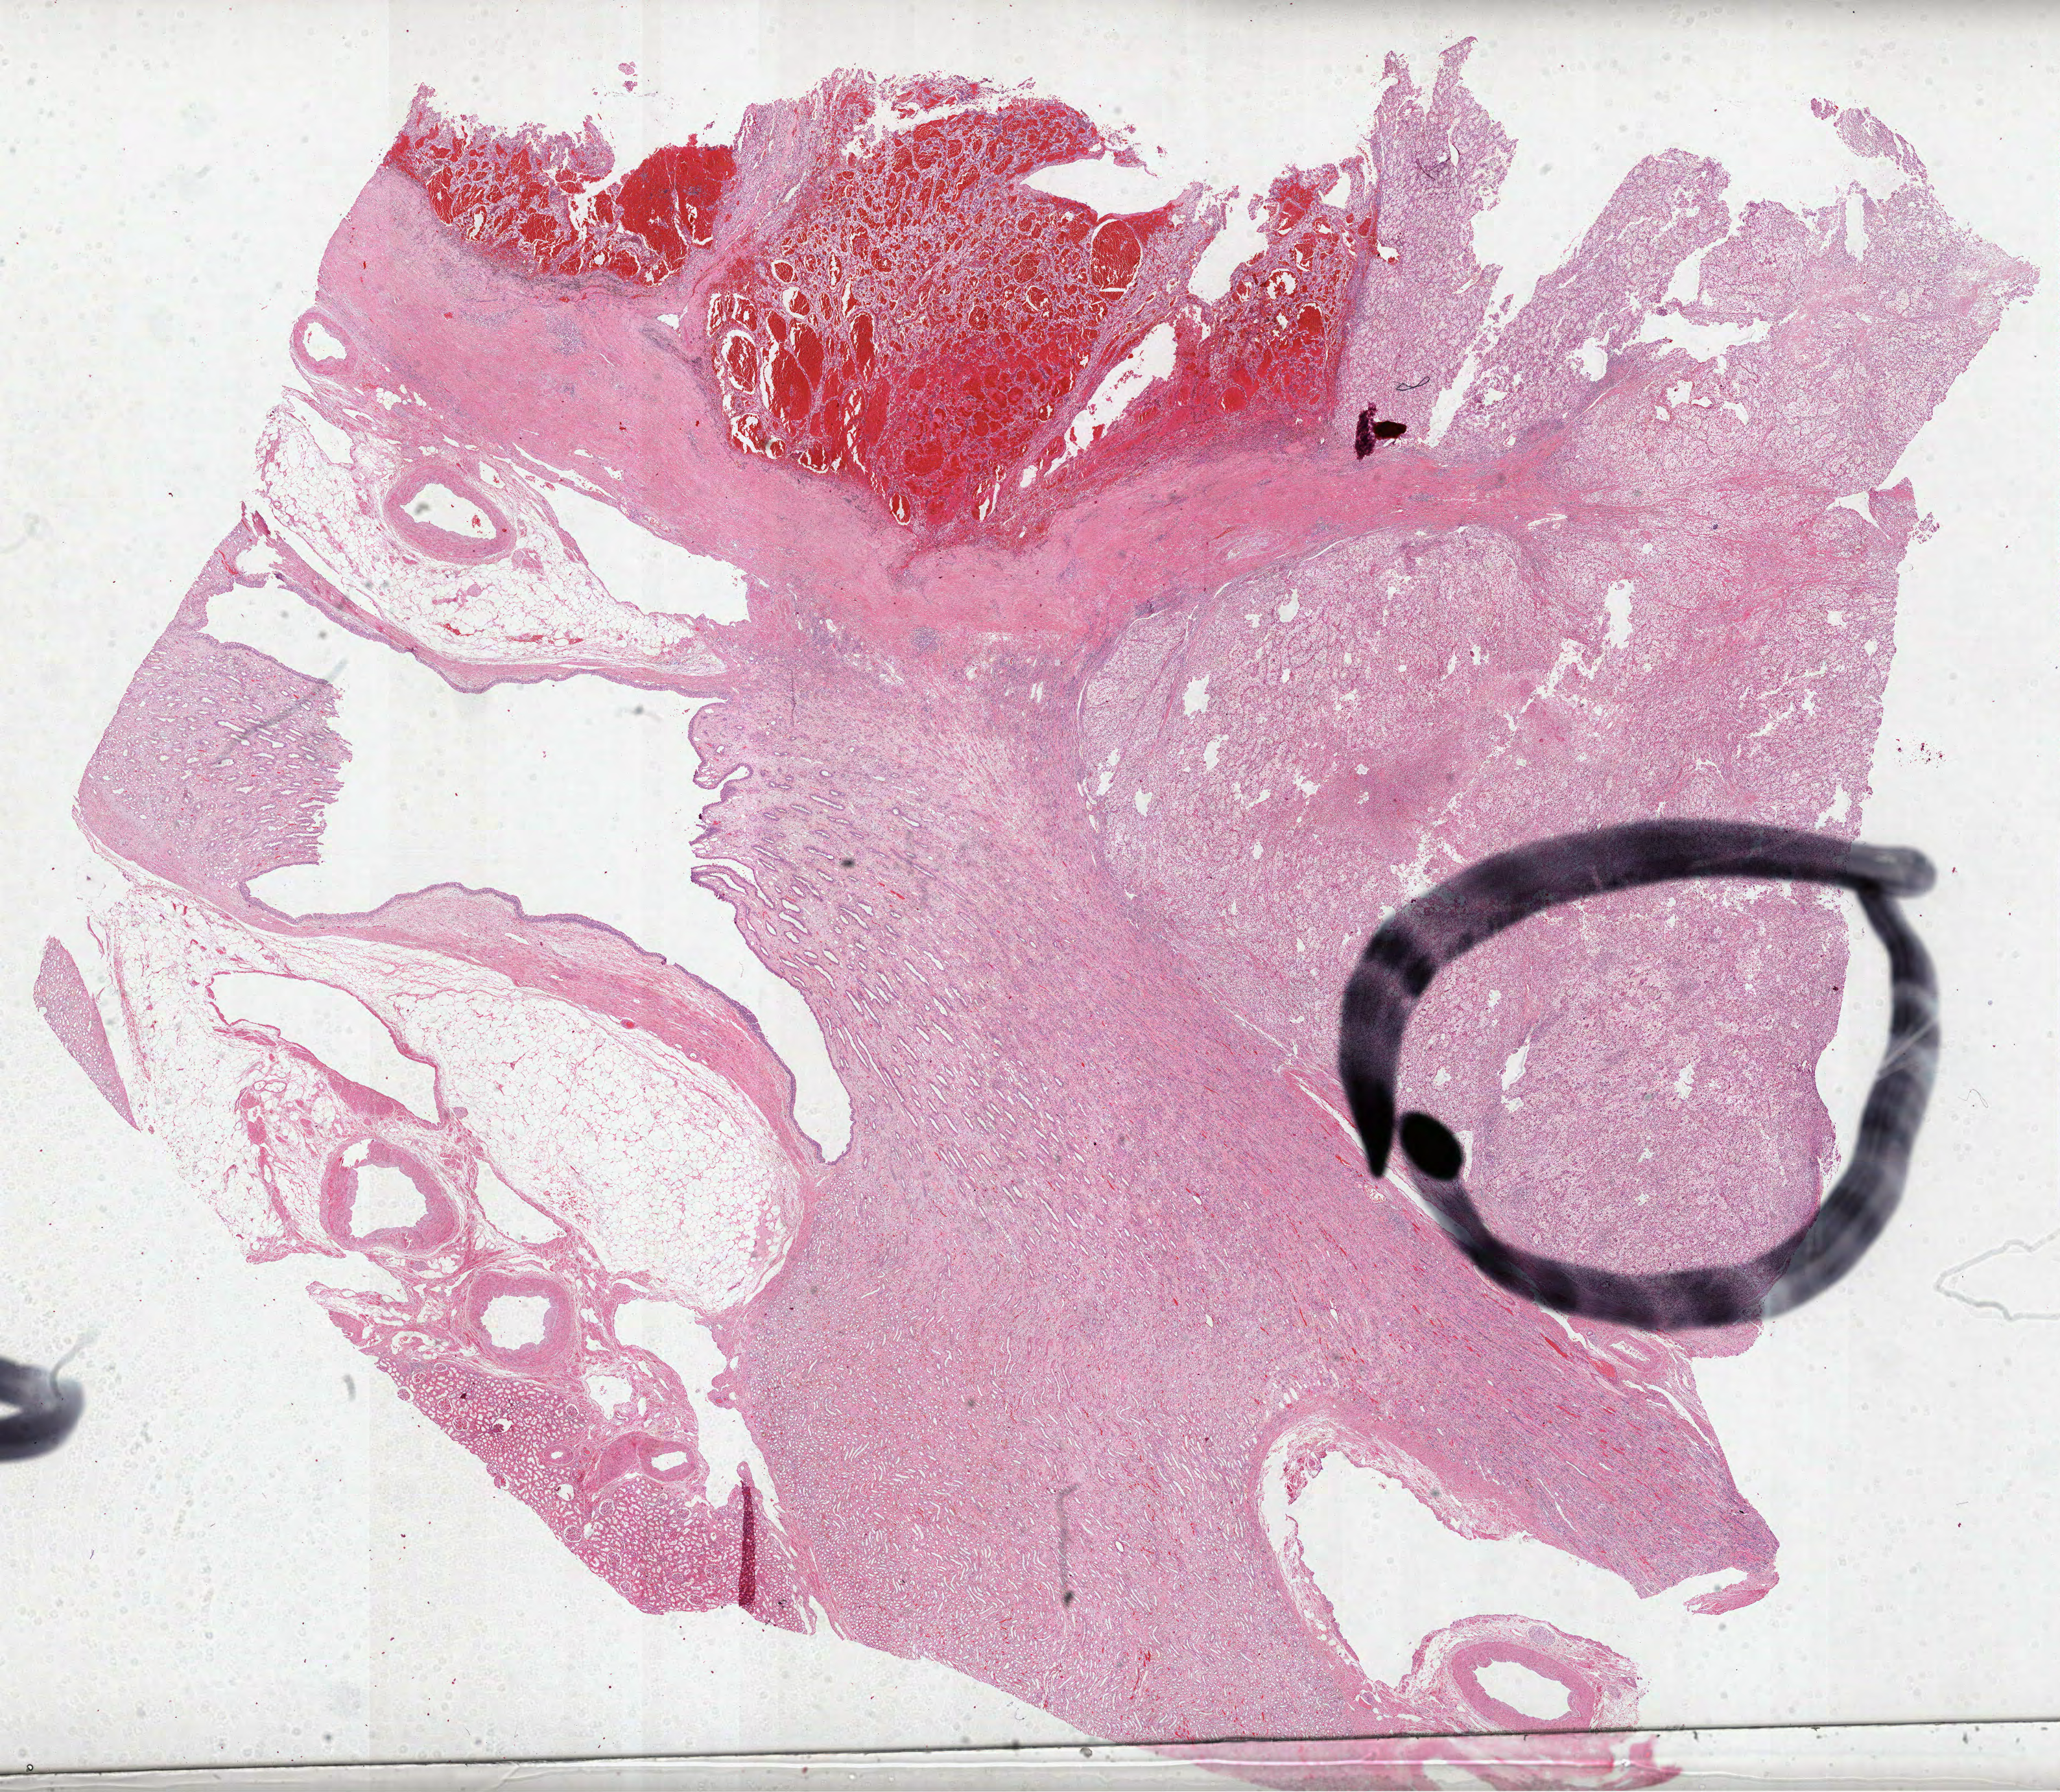
Digitized H&E-stained tissue section (whole slide) — a low-resolution overview of the entire scanned area, about 25.6 x 22.3 mm (slide scanned at 40x), FFPE section, primary tumour sample from the kidney. Female patient; age at initial diagnosis 73 years. Histologic grade: G4 (undifferentiated).
AJCC pathologic stage: III. Diagnosis: Clear cell adenocarcinoma, NOS.